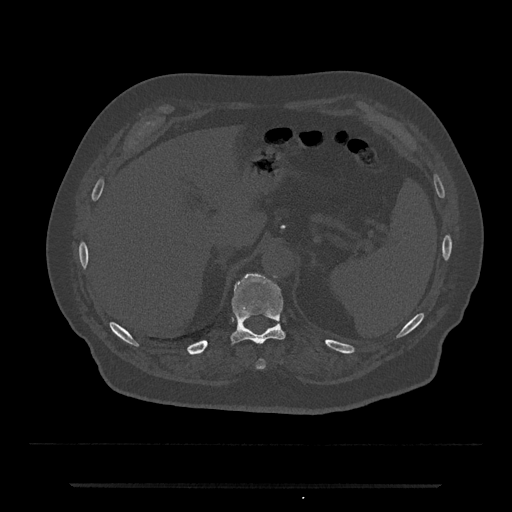
CT including the spine, one axial slice; position 651 of 797 along the scan axis; reconstruction kernel Br40s/3; bone window (W 1800 / L 400 HU); 512 × 512 image matrix. Patient: male, 80 years. From the clinical record (not read from this slice): primary cancer: prostate; vertebrae with lytic lesions (as recorded): L1, T11.
Outlined on this slice (semi-automatically segmented with operator editing):
- T10 vertebra: bounding box <256,359,265,369> (left, top, right, bottom; pixels)
- T11 vertebra: <231,274,285,345>